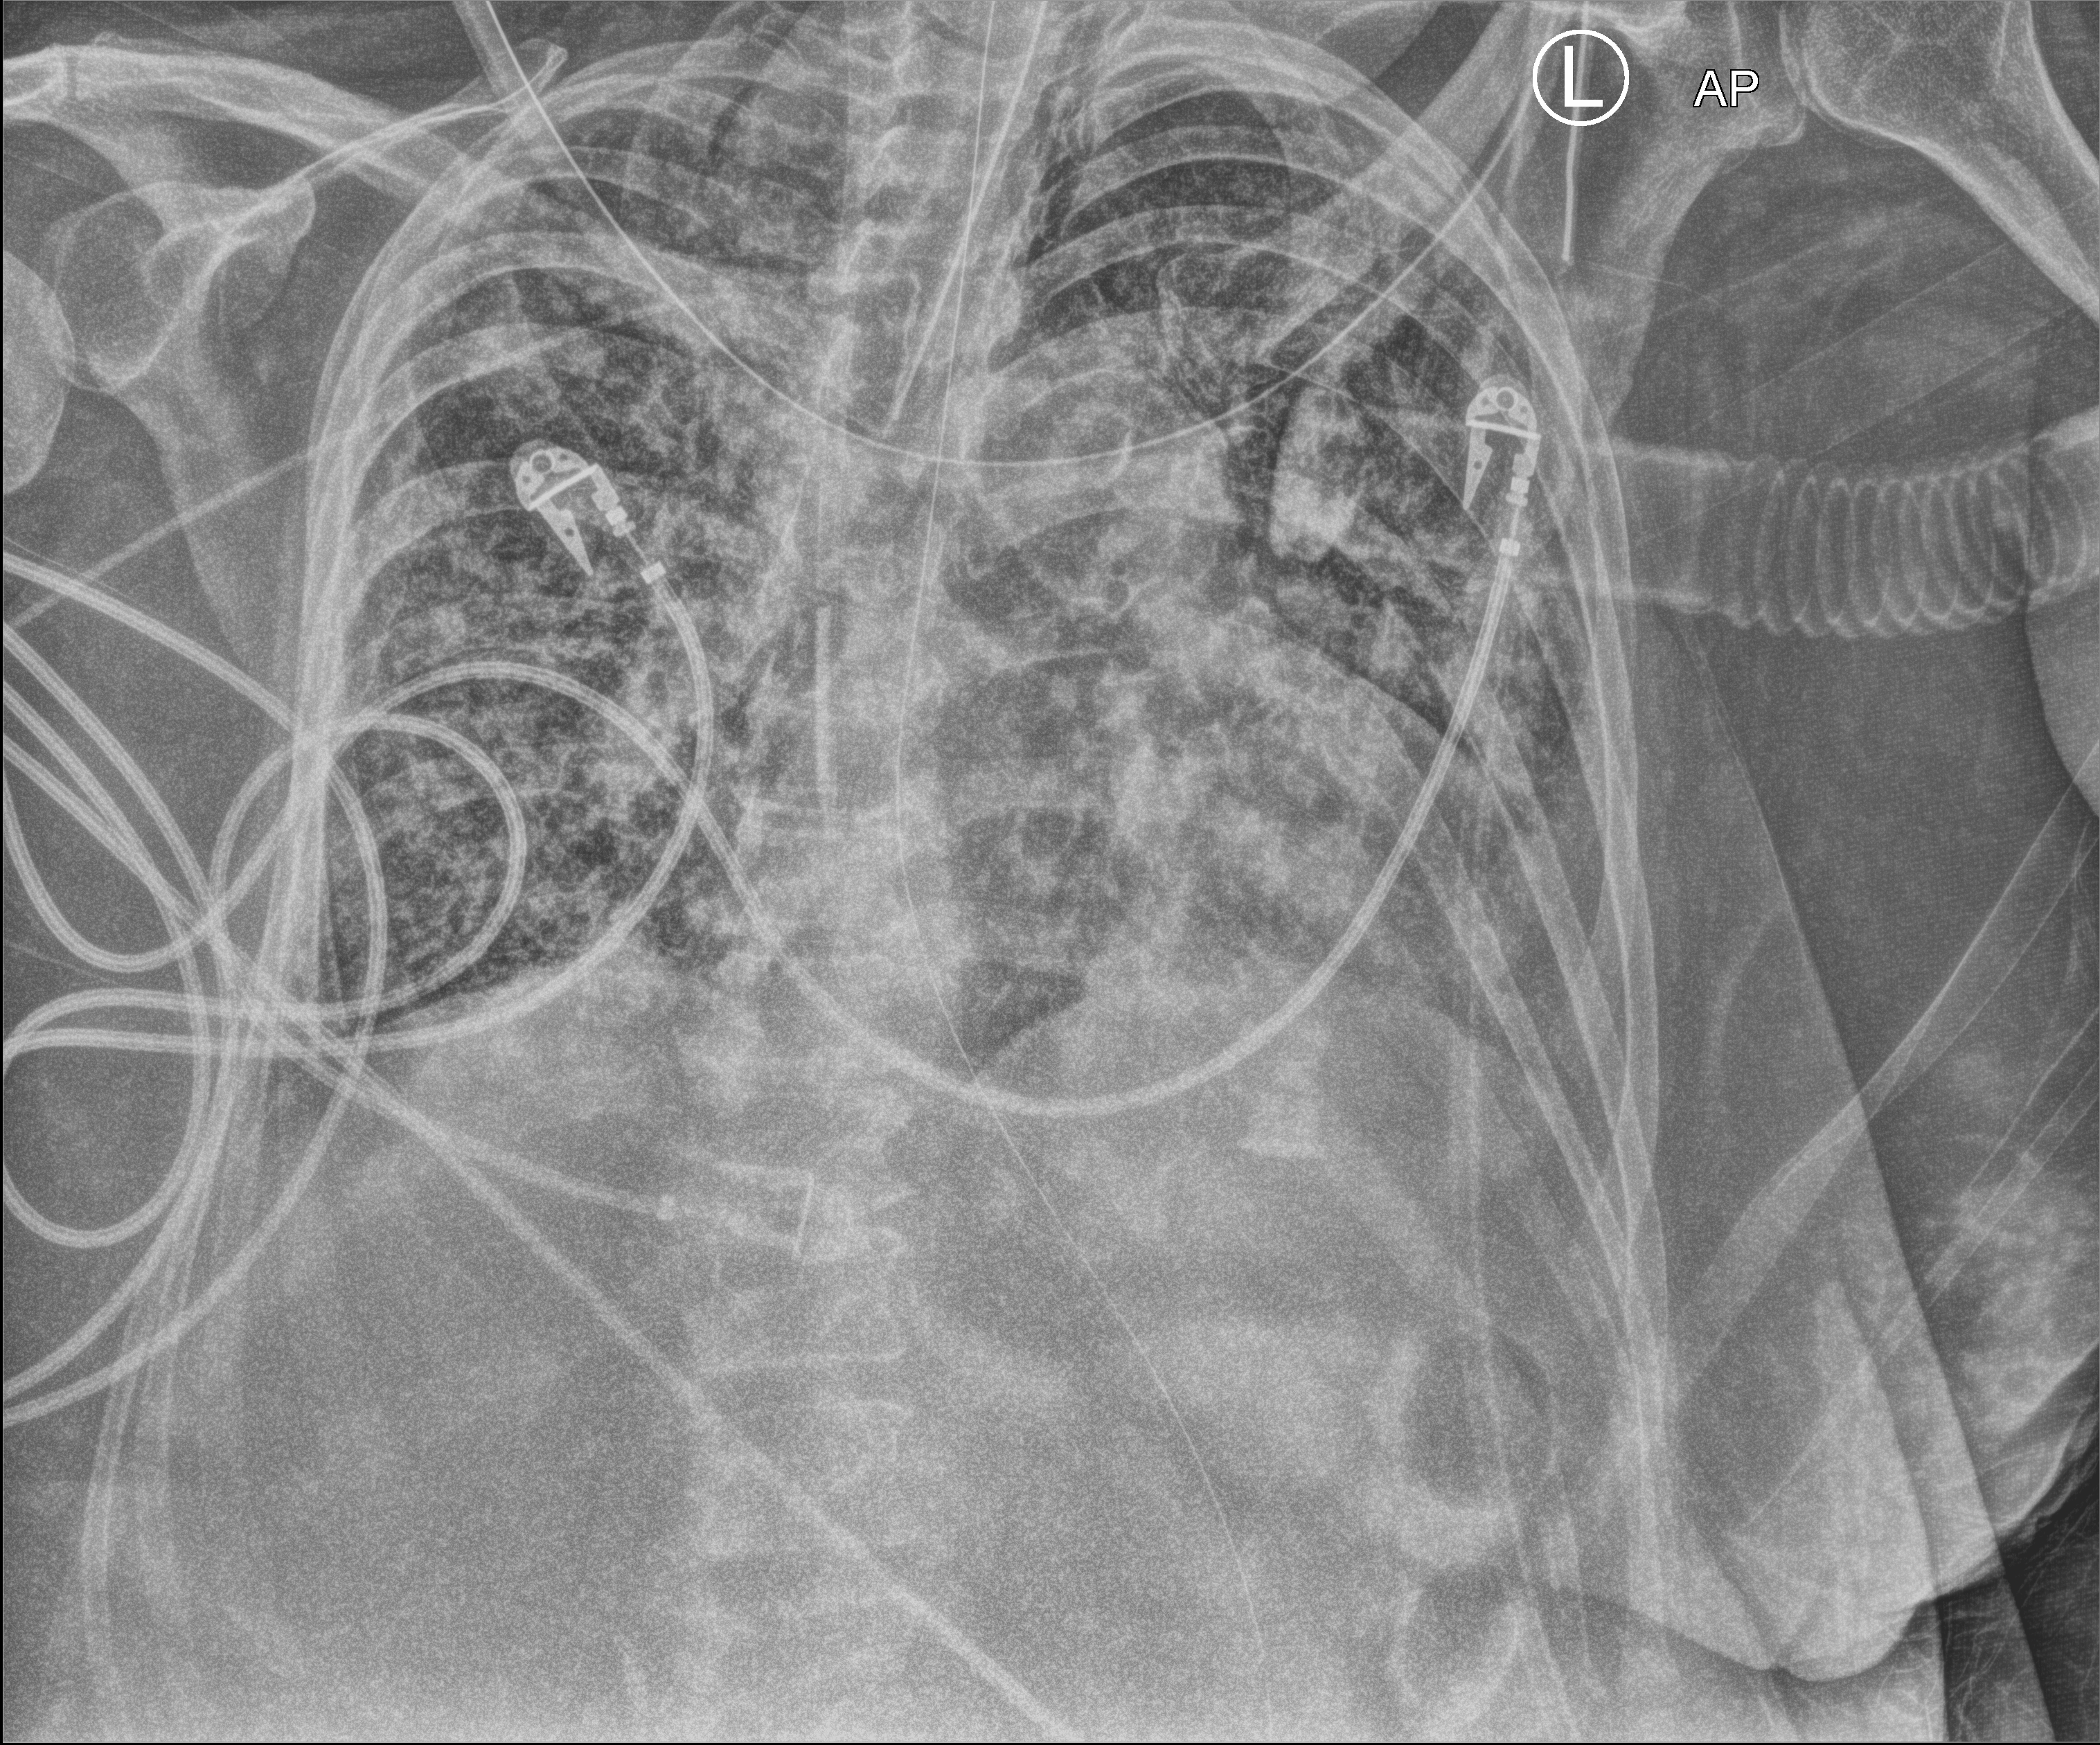
Chest X-ray (portable); anteroposterior (AP) projection. Patient hospitalised with COVID-19; female, aged 60–74 years.
Admission-level facts for this patient (not findings on this image; timing relative to this image not recorded):
- mechanically ventilated during this hospital stay: yes
- hypertension (admission record): yes
- admitted to intensive care during this hospital stay: yes